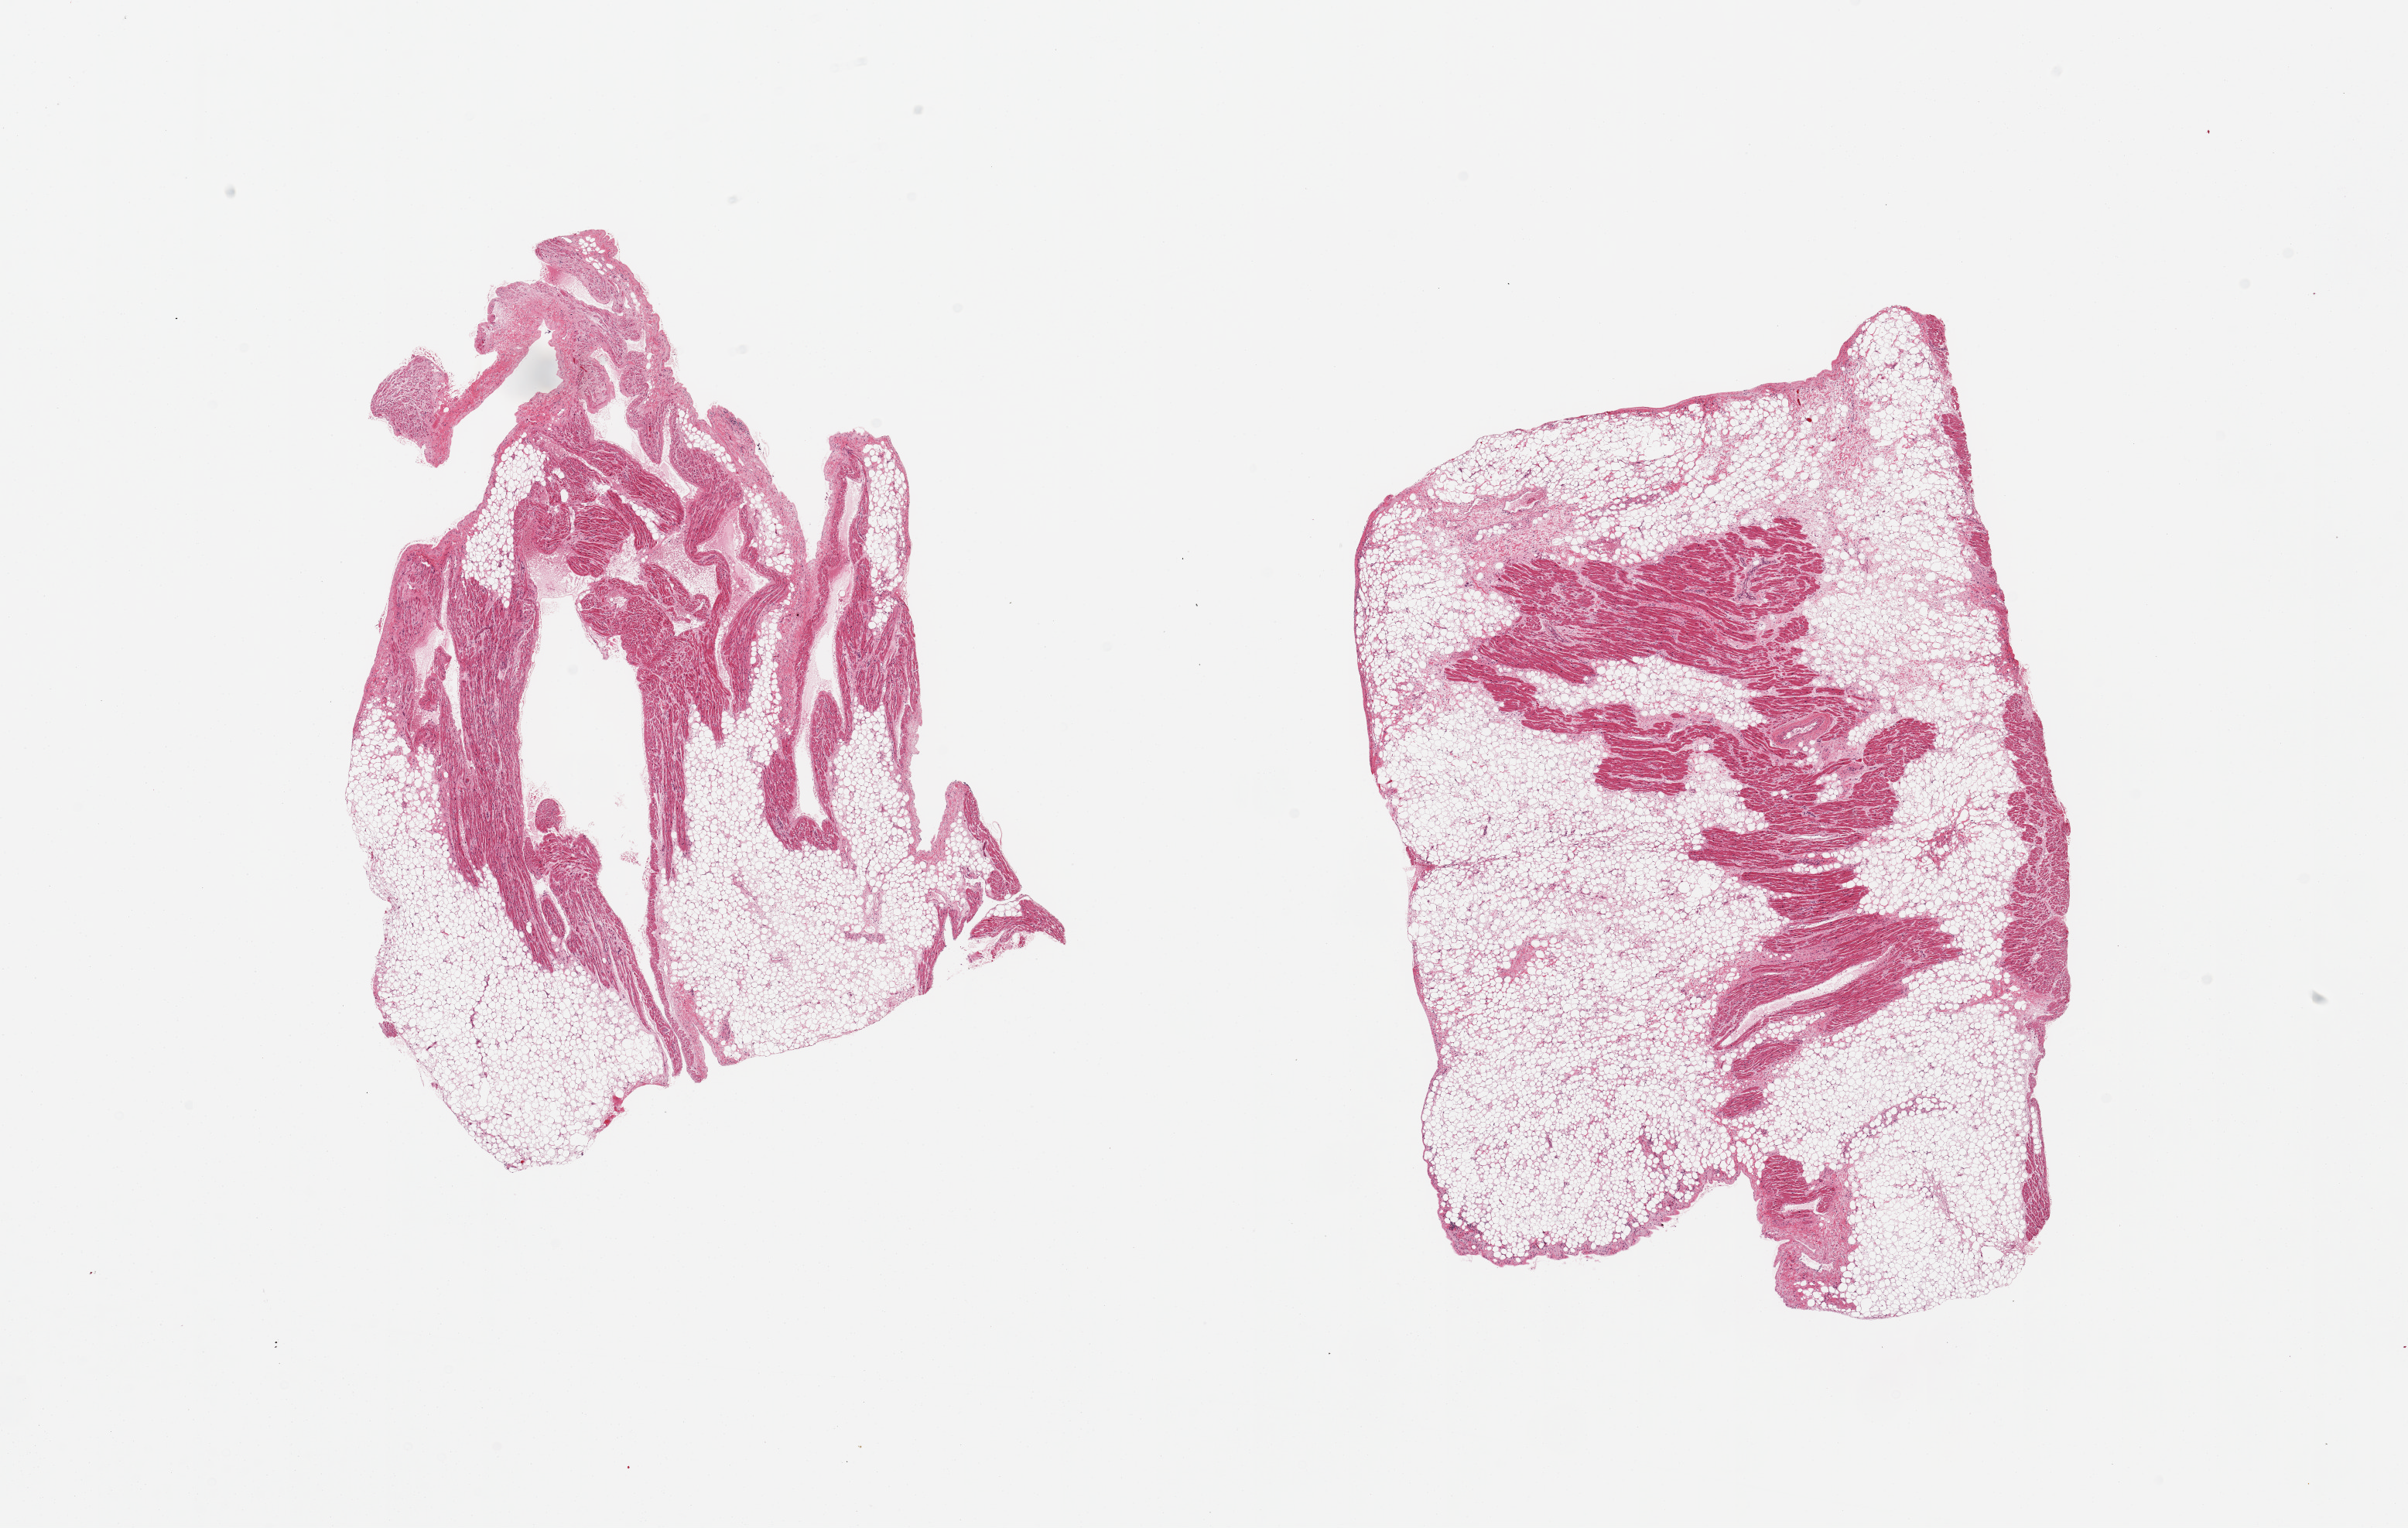
Digitized H&E-stained section — shown as a low-resolution overview of the whole scanned area (about 24.6 x 15.6 mm, slide scanned at 20x). PAXgene-fixed, paraffin-embedded tissue. Sampled site (target tissue): auricular appendage. Donor tissue sample. Donor sex: female.
Review note (as recorded): 2 pieces; 50 & 80% fat.